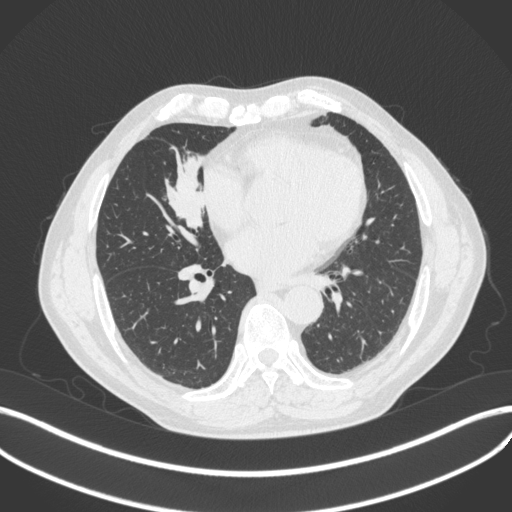
Chest CT, one axial slice; position 173 of 429 along the scan axis; reconstruction kernel B31f; 120 kVp; lung window (W 1500 / L -600 HU); 1 mm slice thickness; 512 × 512 image matrix. Patient: male, 61 years. From the clinical record (not read from this slice): clinical TNM (as recorded): T2b N1 M0.
Outlined on this slice (bounding box drawn by a radiologist):
- lung tumour (recorded histology: squamous cell carcinoma): bounding box (x1, y1, x2, y2) in pixels: (156, 143, 212, 237)